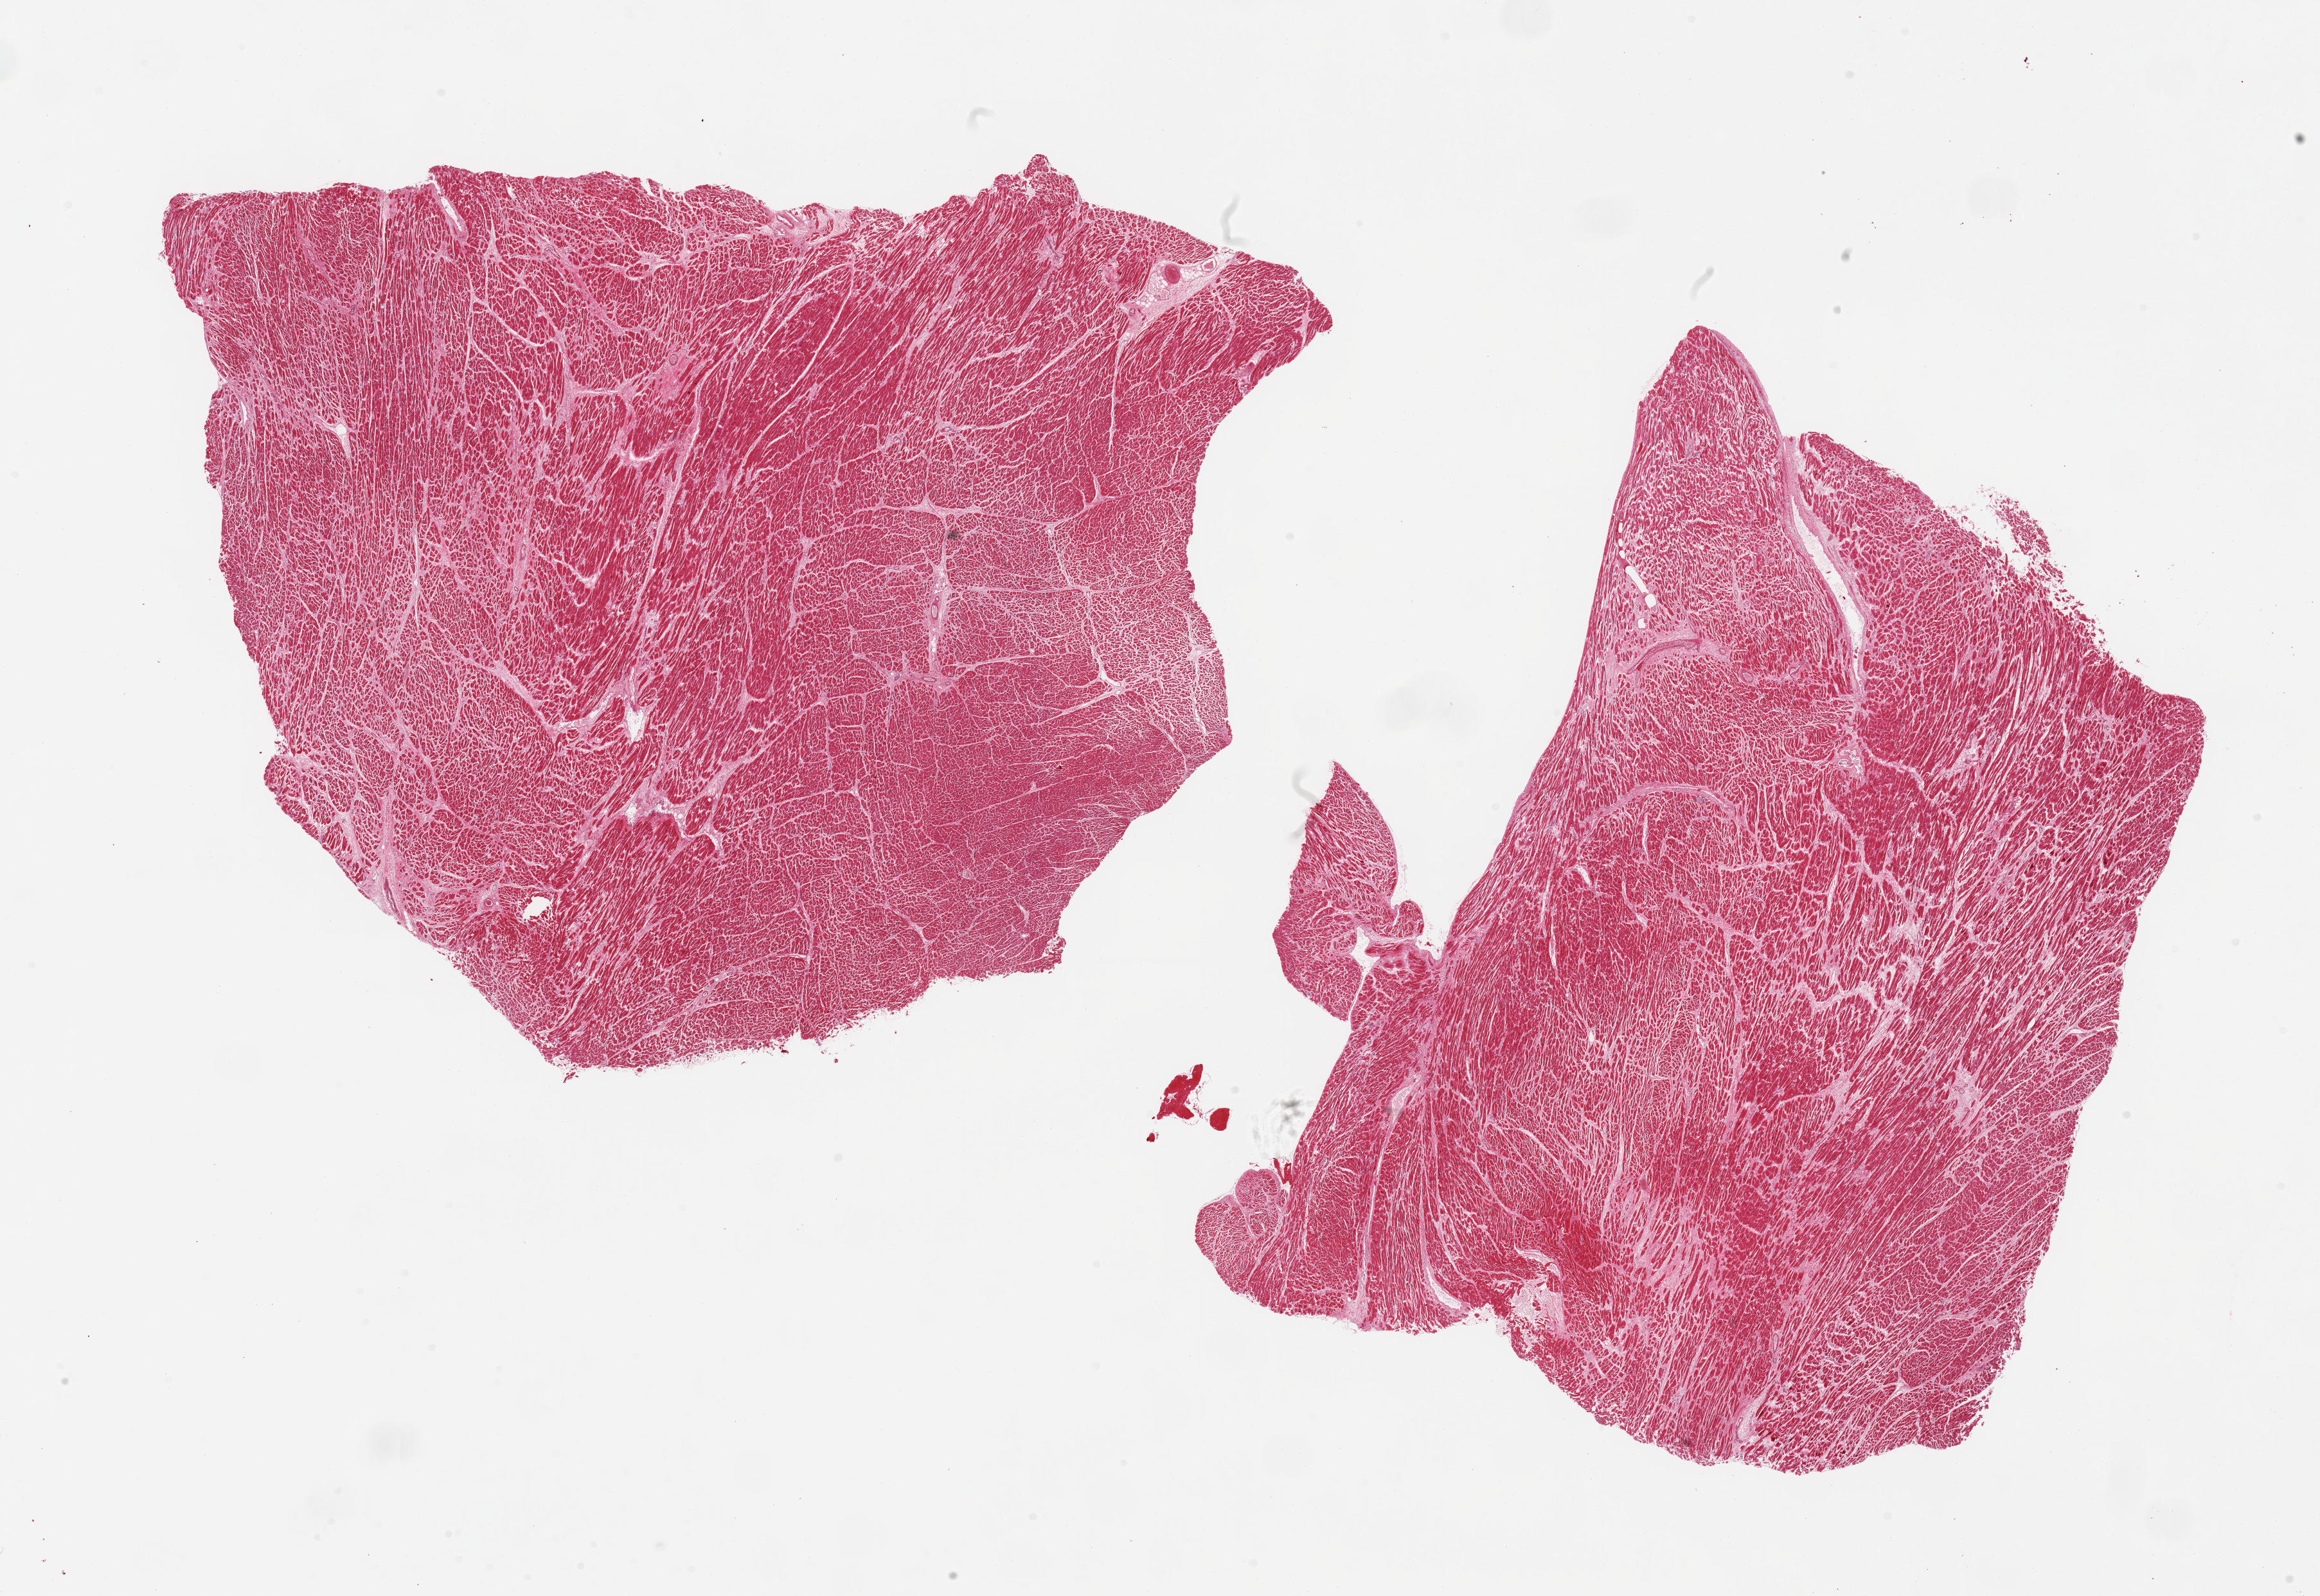
H&E whole-slide image — low-resolution overview of the scanned area, about 28.5 x 19.6 mm, PAXgene-fixed paraffin-embedded (PFPE) section, section of heart (target tissue), tissue donor sample. Donor sex: male.
Reviewer comment on this tissue sample: 2 pieces, diffuse moderate-marked chronic ischemic changes/intersitital fibrosis.